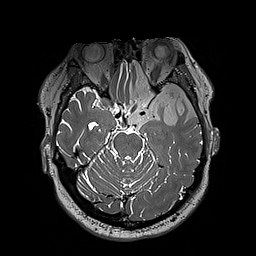
Brain MRI from a brain-tumour surgery series, one axial slice; position 135 of 192 along the scan axis; 256 × 256 image matrix, field of view 250 × 250 mm. Case-level facts recorded for this patient, not image findings: histopathology: Oligodendroglioma; WHO grade: 3; IDH mutation: yes.
Structures marked on this image (expert manual segmentation):
- tumour: bounding box <124,60,197,126> (left, top, right, bottom; pixels)